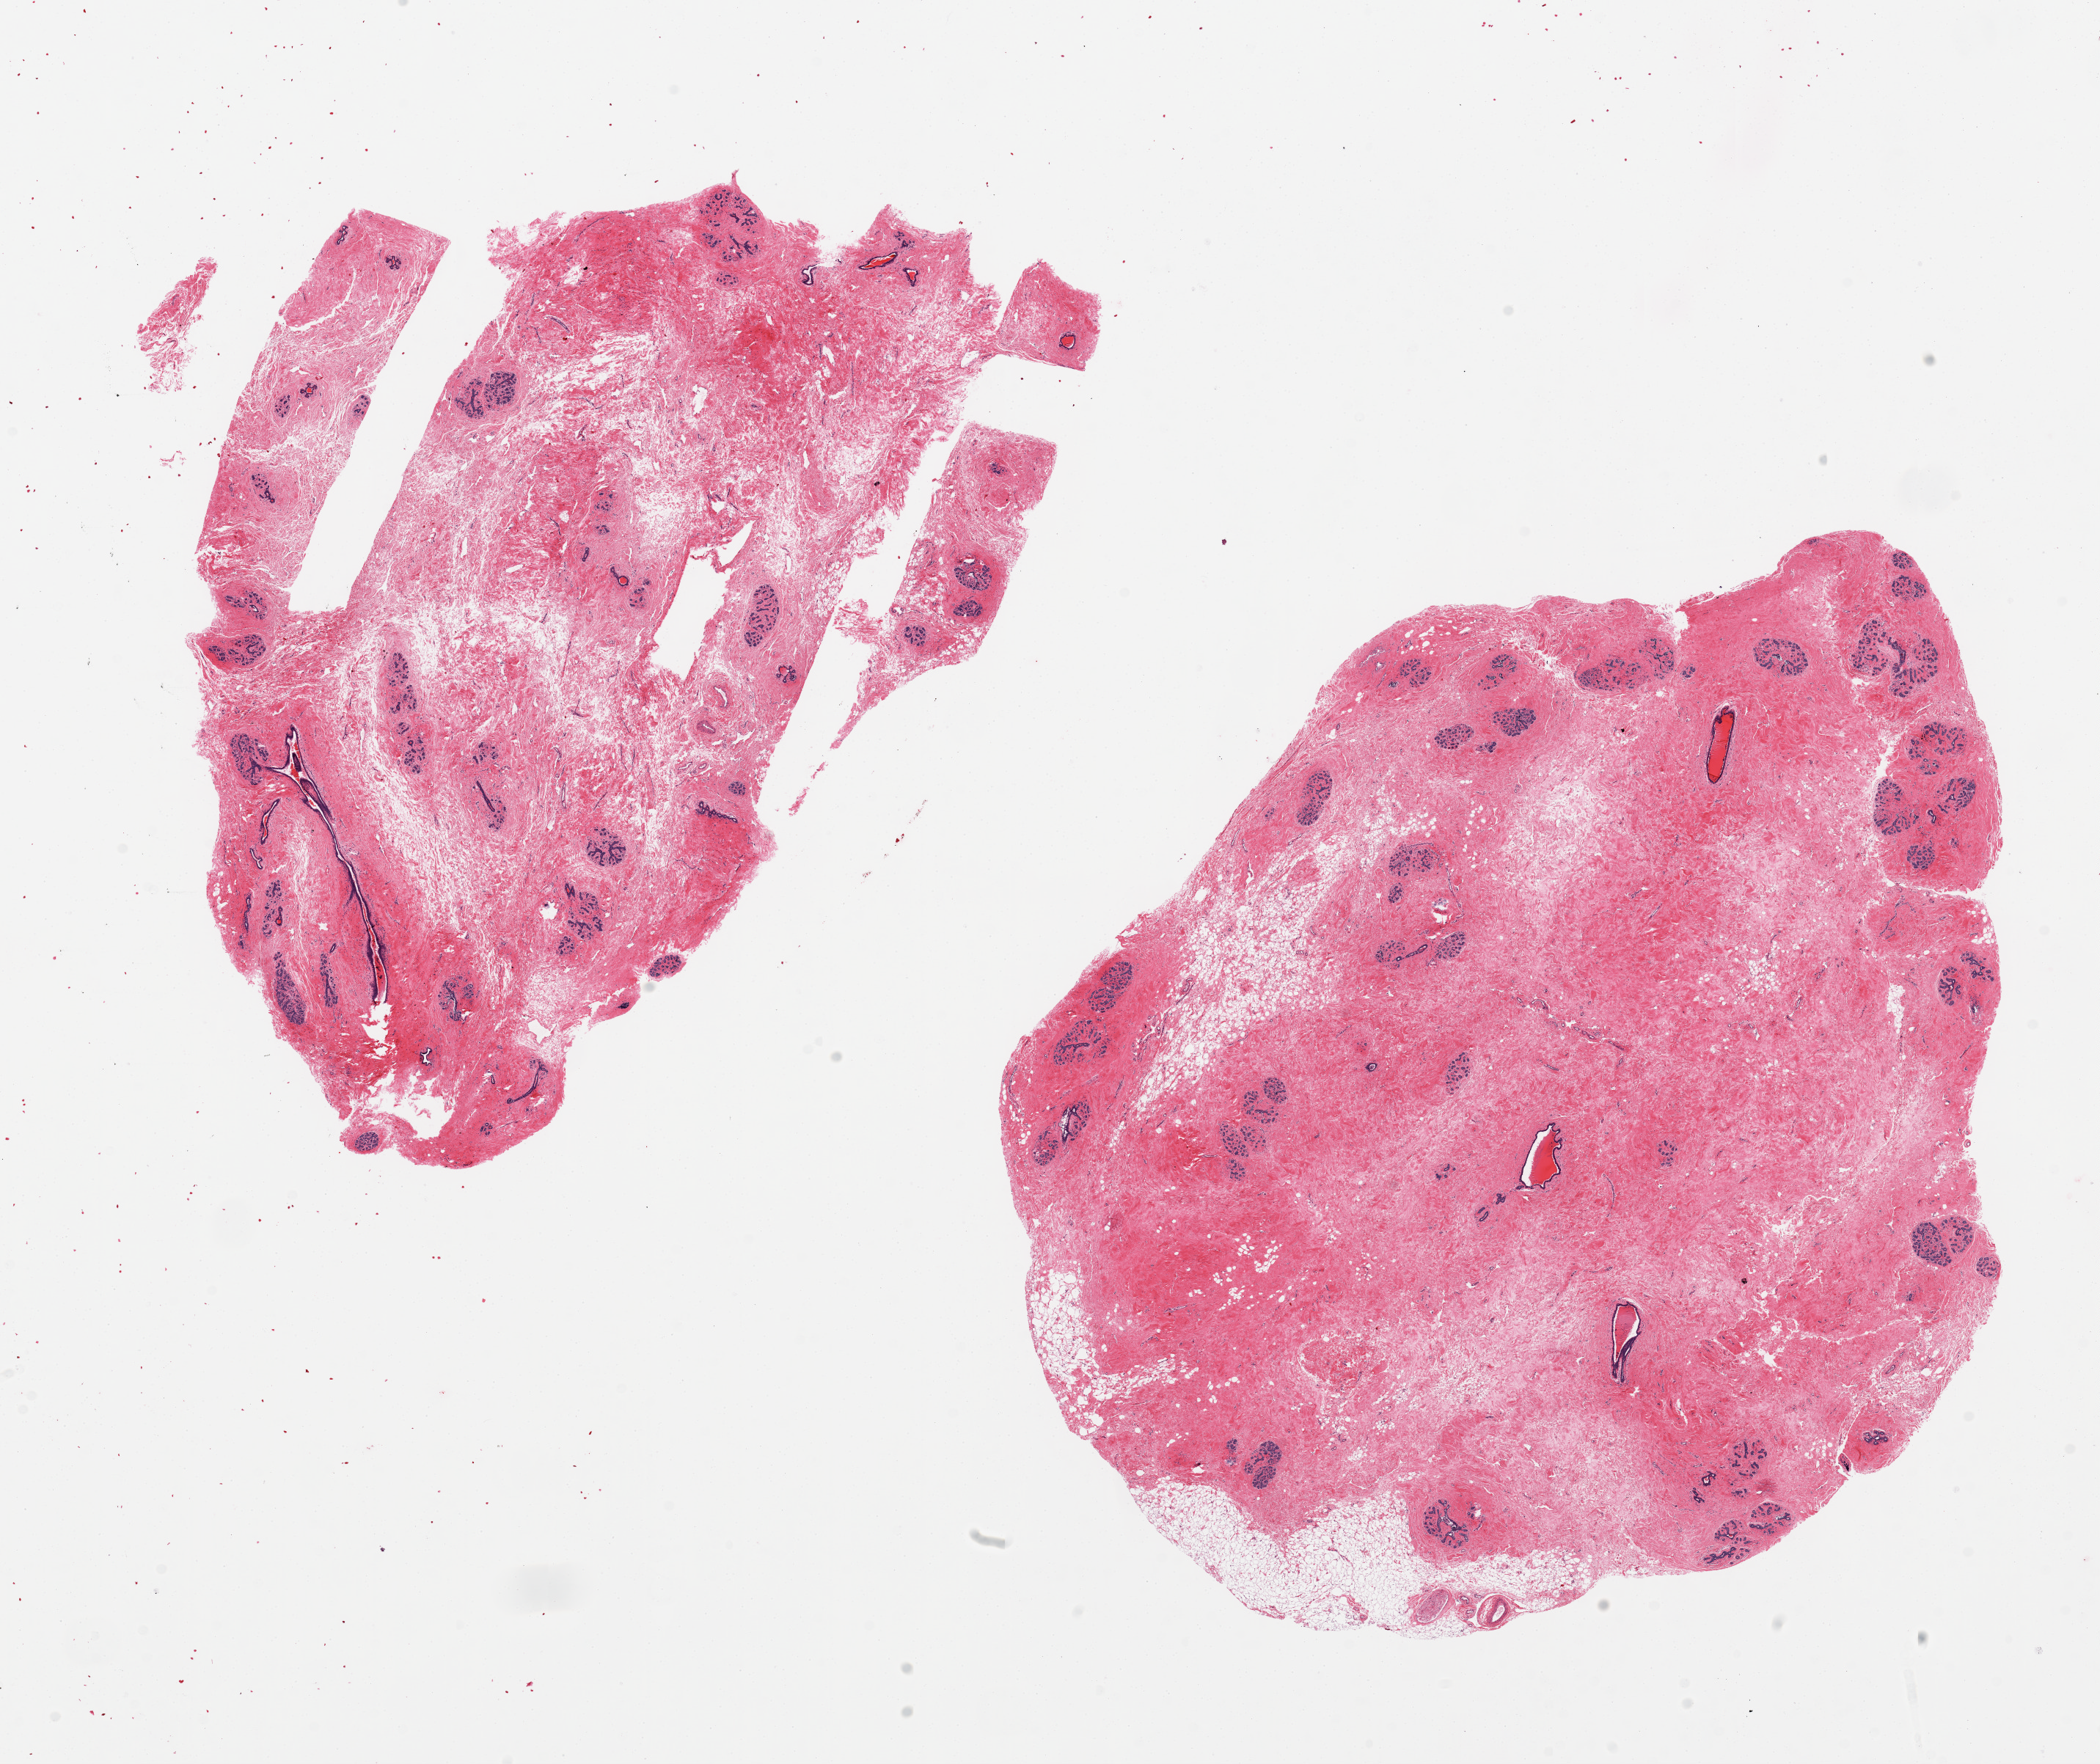
Haematoxylin and eosin whole-slide image — low-resolution overview of the scanned area, about 22.6 x 19.0 mm. PAXgene-fixed, paraffin-embedded tissue. Sampled site (target tissue): breast. Donor tissue sample. Donor: female.
- review note (as recorded): 2 pieces, predominantly fibrous stroma with many ducts/lobules